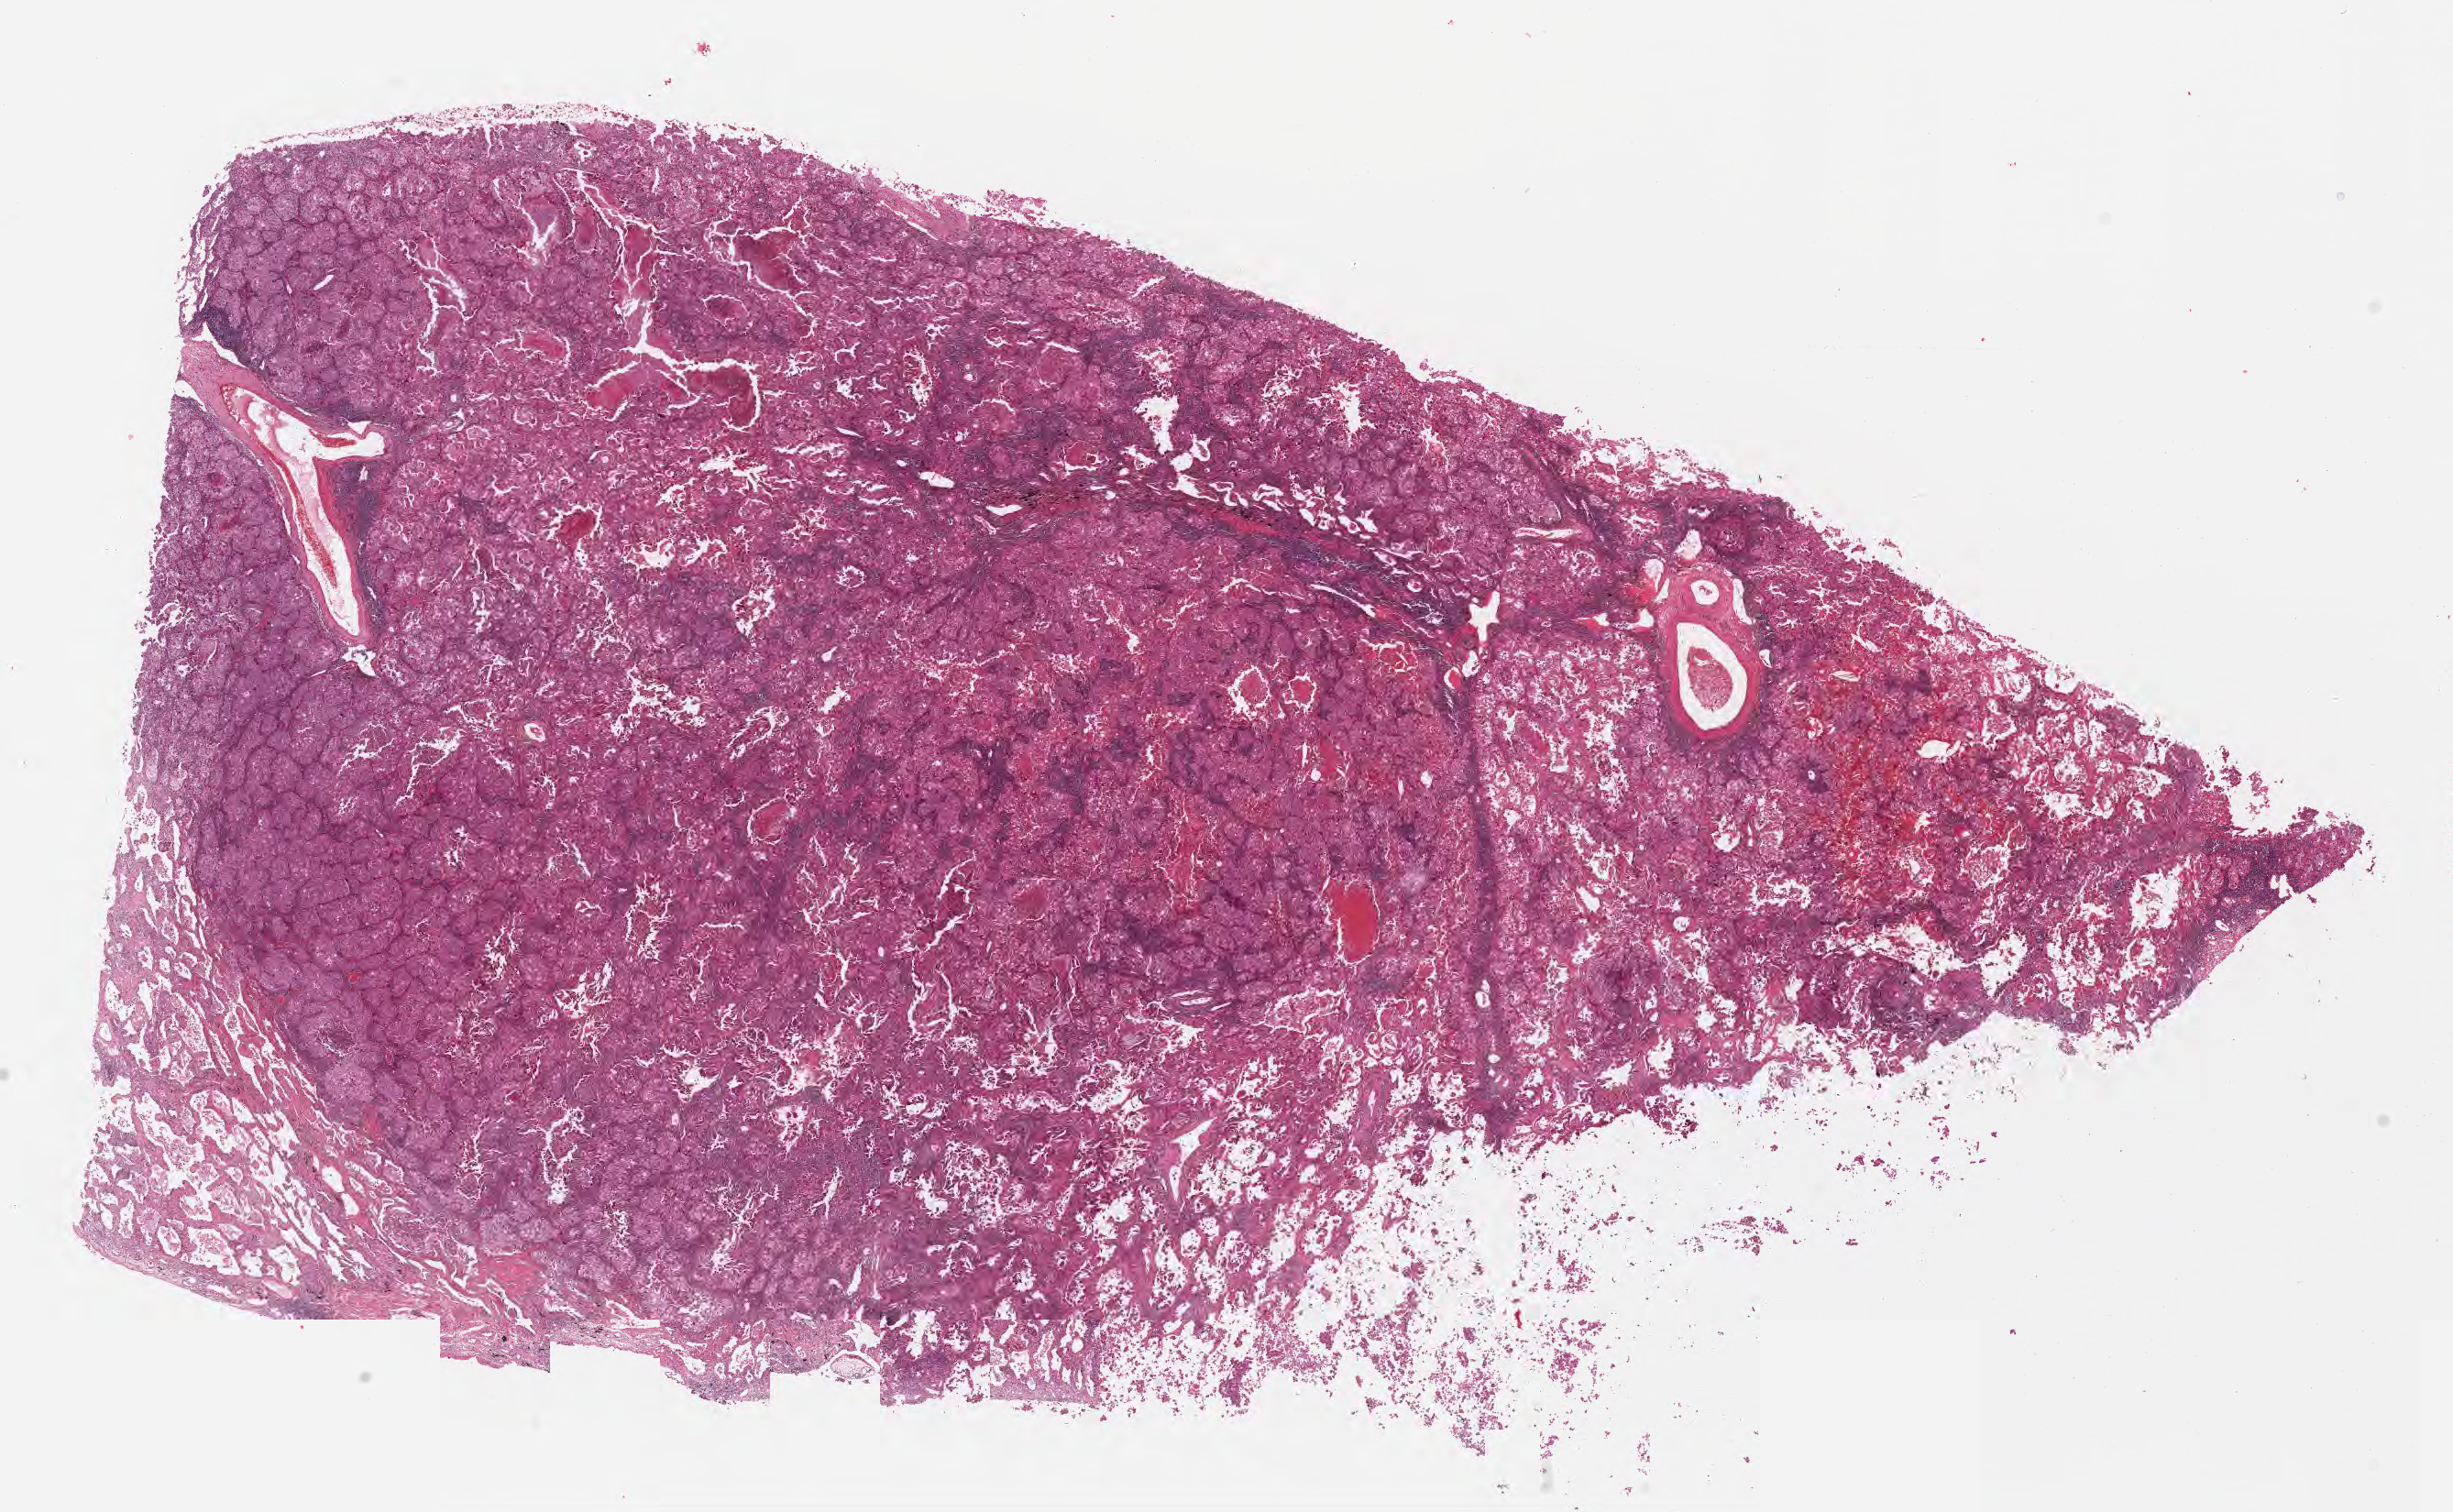
Whole-slide image, haematoxylin and eosin stain — low-resolution overview of the scanned area, about 21.6 x 13.3 mm. FFPE section. Specimen: primary tumor. Site: middle lobe of right lung. Male patient, 65 years old.
Diagnosis: Adenocarcinoma, NOS.